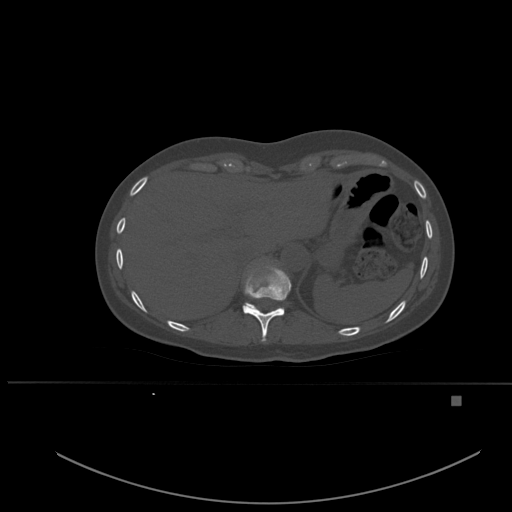
CT including the spine, one axial slice. Bone window (W 1800 / L 400 HU). 1.5 mm slice thickness. 512 × 512 image matrix, field of view 443 × 443 mm. Patient: female, 49 years. Case-level facts recorded for this patient, not image findings: primary cancer: breast.
Outlined on this slice (semi-automatic segmentation, software-assisted and operator-edited):
- T10 vertebra: bounding box [x1, y1, x2, y2] px = [243, 265, 291, 342]
- T11 vertebra: [247, 303, 279, 311]